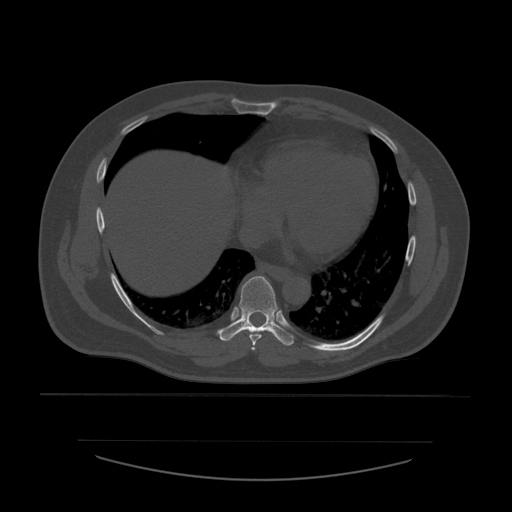
CT including the spine, one axial slice. Slice 343 of 532 in the series (ordered by position). Bone window (W 1800 / L 400 HU). 1.25 mm slice thickness. 512 × 512 image matrix, field of view 441 × 441 mm. Patient age 44 years. Case-level facts recorded for this patient, not image findings: primary cancer: soft tissue sarcoma.
Structures marked on this image (semi-automatic segmentation, software-assisted and operator-edited):
- T6 vertebra: bounding box (x1, y1, x2, y2) in pixels: (252, 347, 256, 351)
- T7 vertebra: (249, 333, 262, 346)
- T8 vertebra: (217, 276, 295, 346)